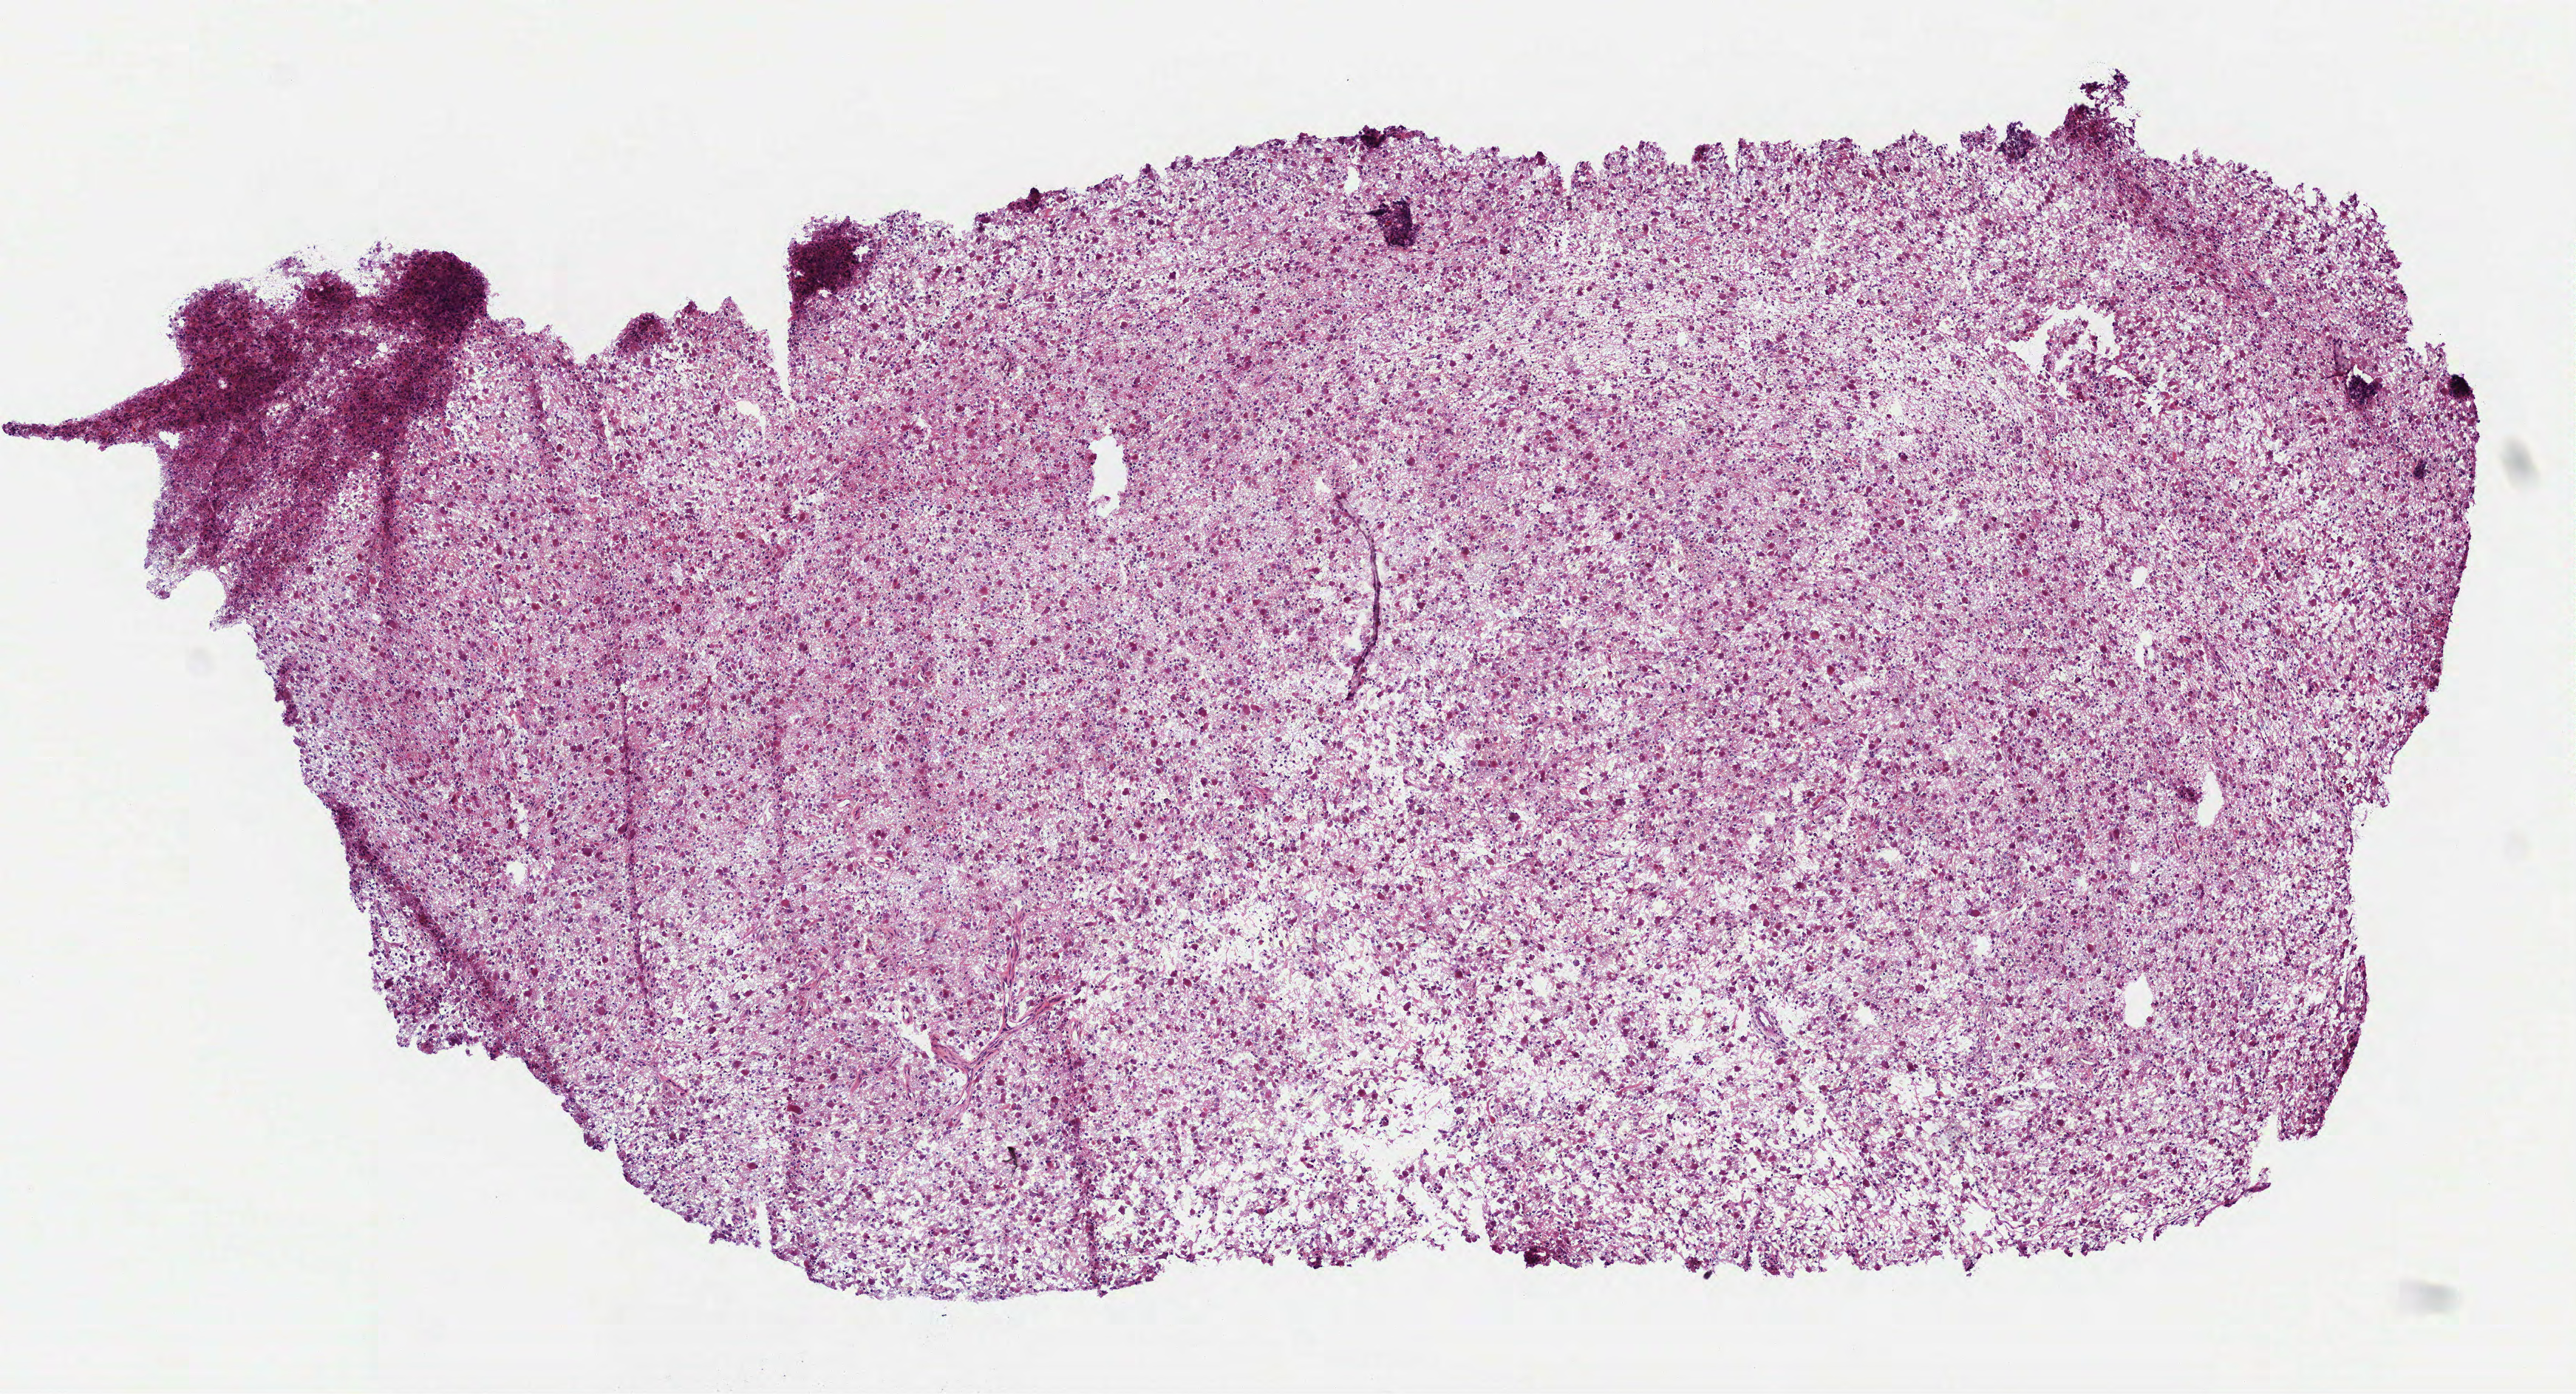
Whole-slide histology image, H&E-stained — whole scanned area (about 7.0 x 3.8 mm, acquisition: 40x scan) shown as a low-resolution overview; frozen section from the top of the tissue portion; brain, primary tumour sample. Female patient; age at initial diagnosis 30 years. Histologic grade: G3 (poorly differentiated). Pathologist review of this section (percent, as recorded): tumour cells 100%, tumour nuclei 85%, normal cells 0%, stromal cells 0%, necrosis 0%.
Laterality: right. Diagnosis: Astrocytoma, anaplastic (cerebrum).